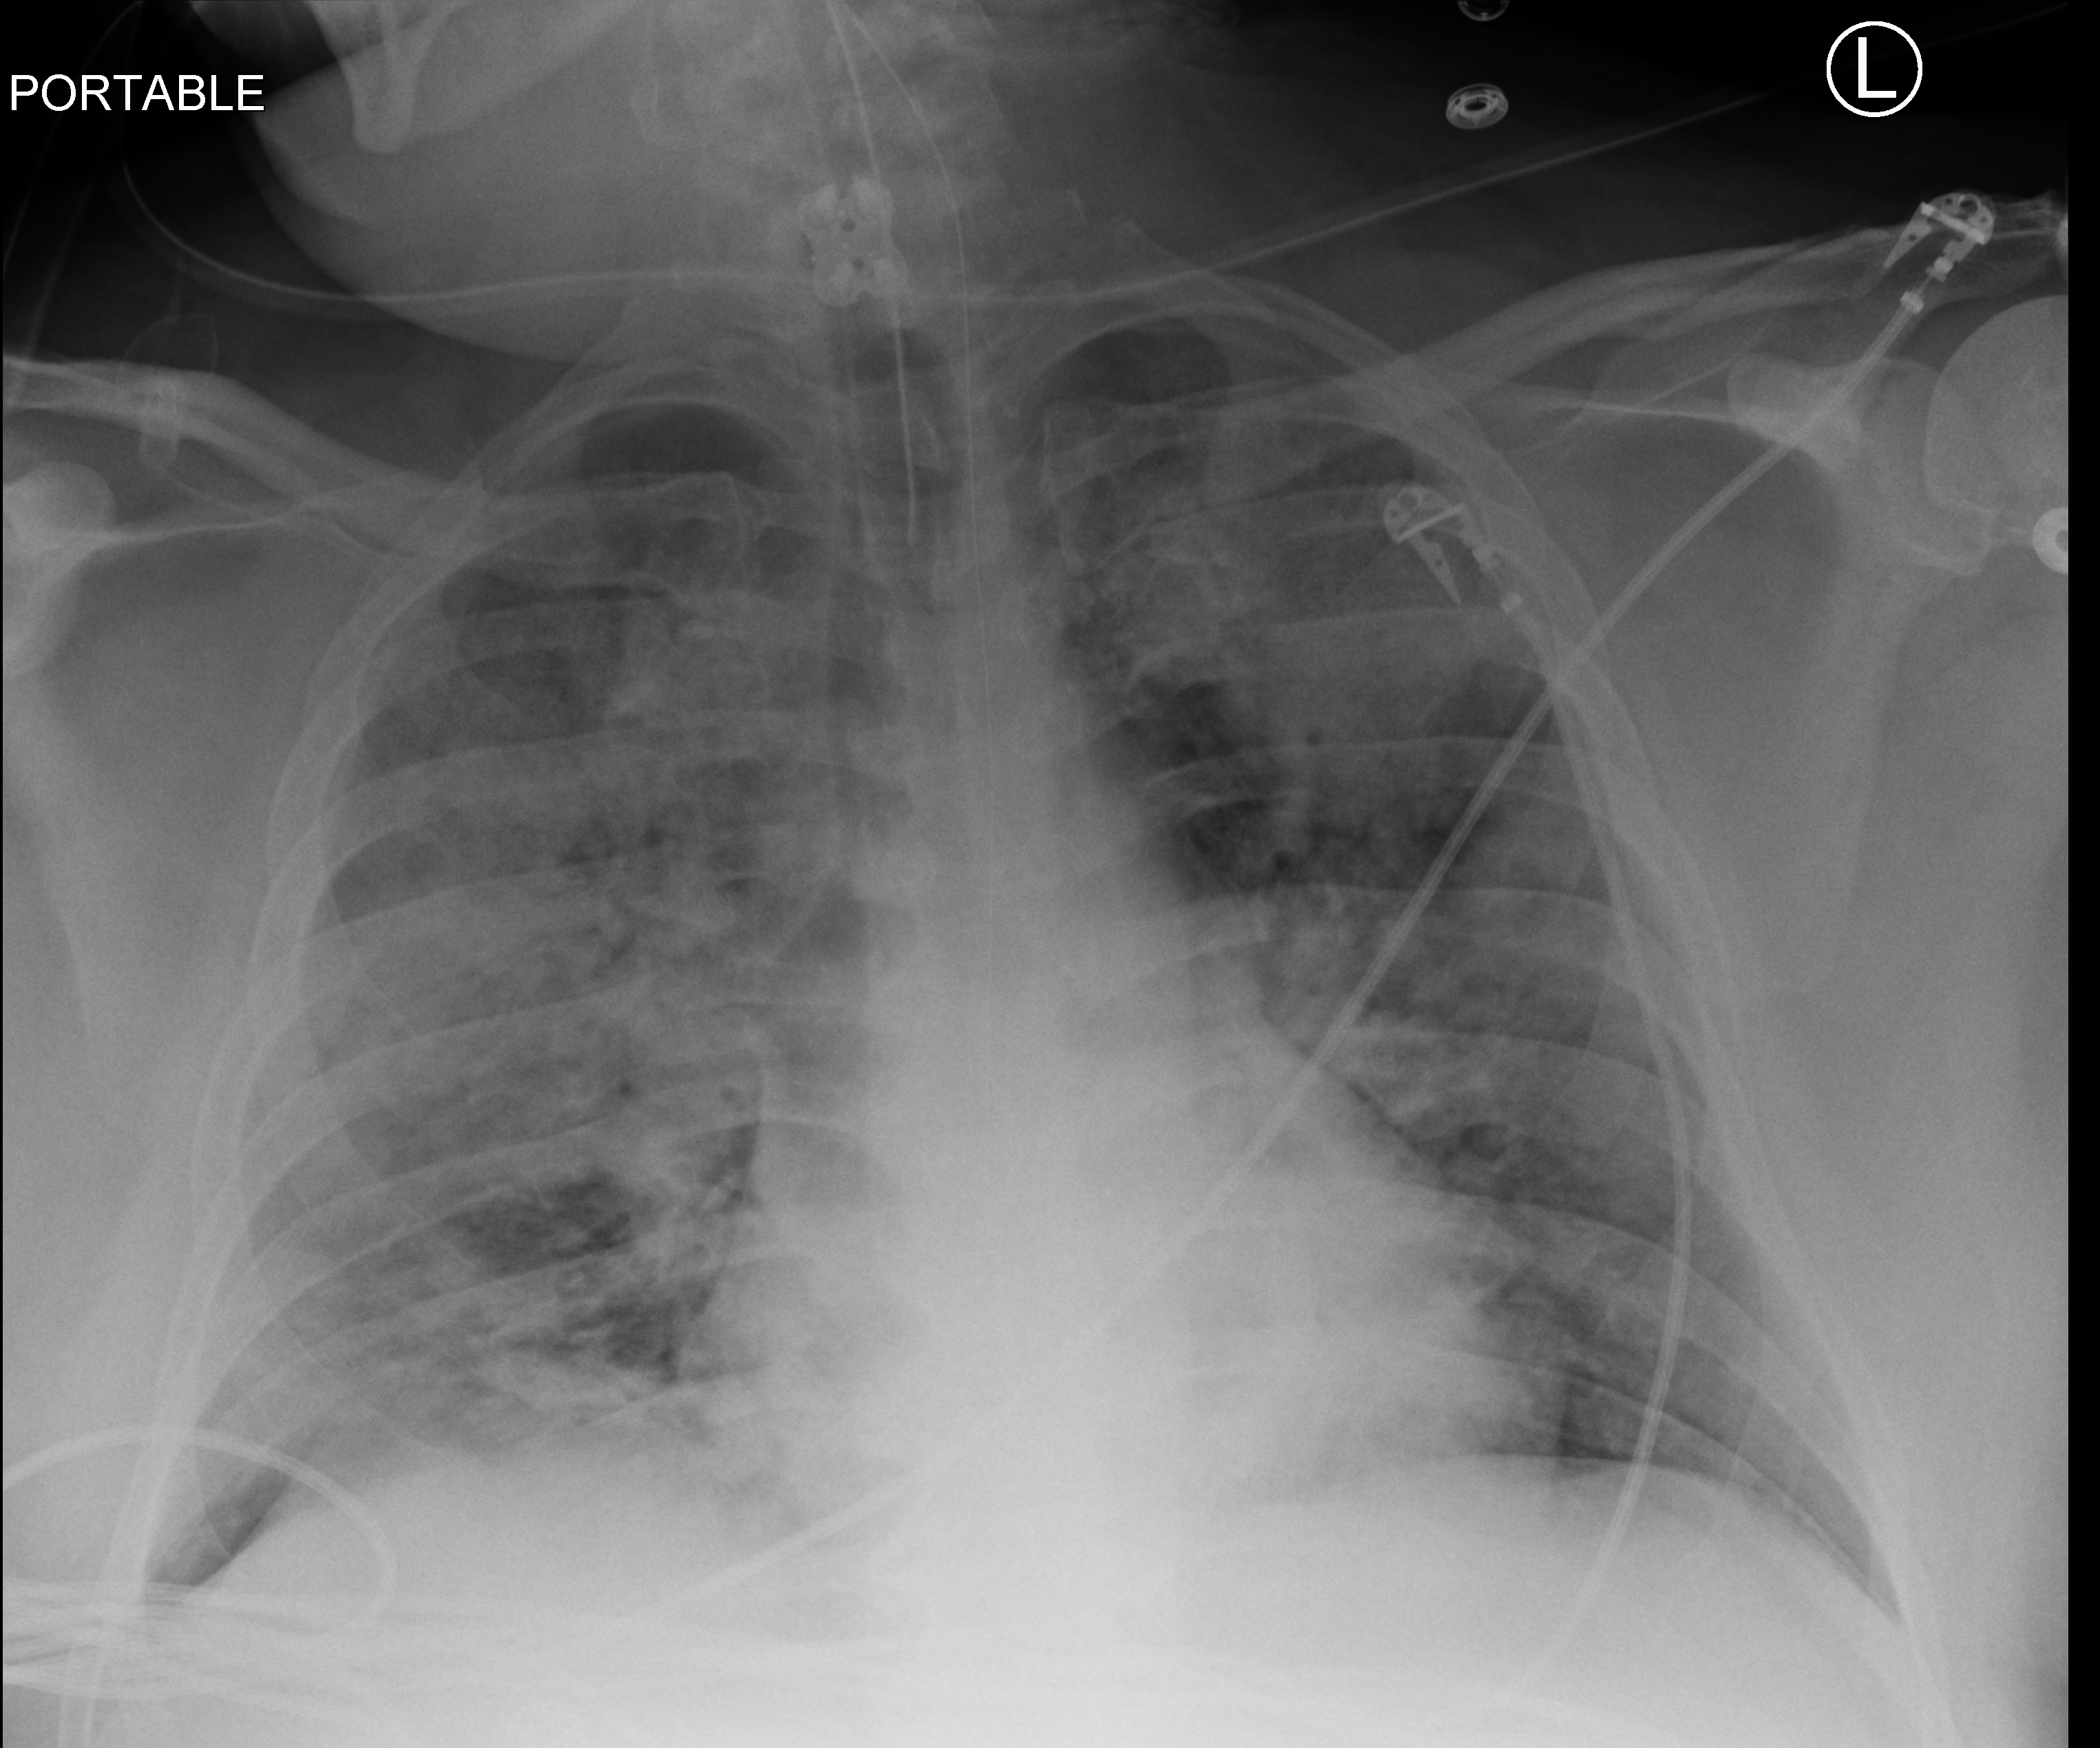
Chest X-ray (portable), anteroposterior (AP) projection. Patient hospitalised with COVID-19; male, aged 18–59 years.
From the hospital-stay record, not from the radiograph (when in the stay this image was taken is not recorded): smoking status (admission record): never.